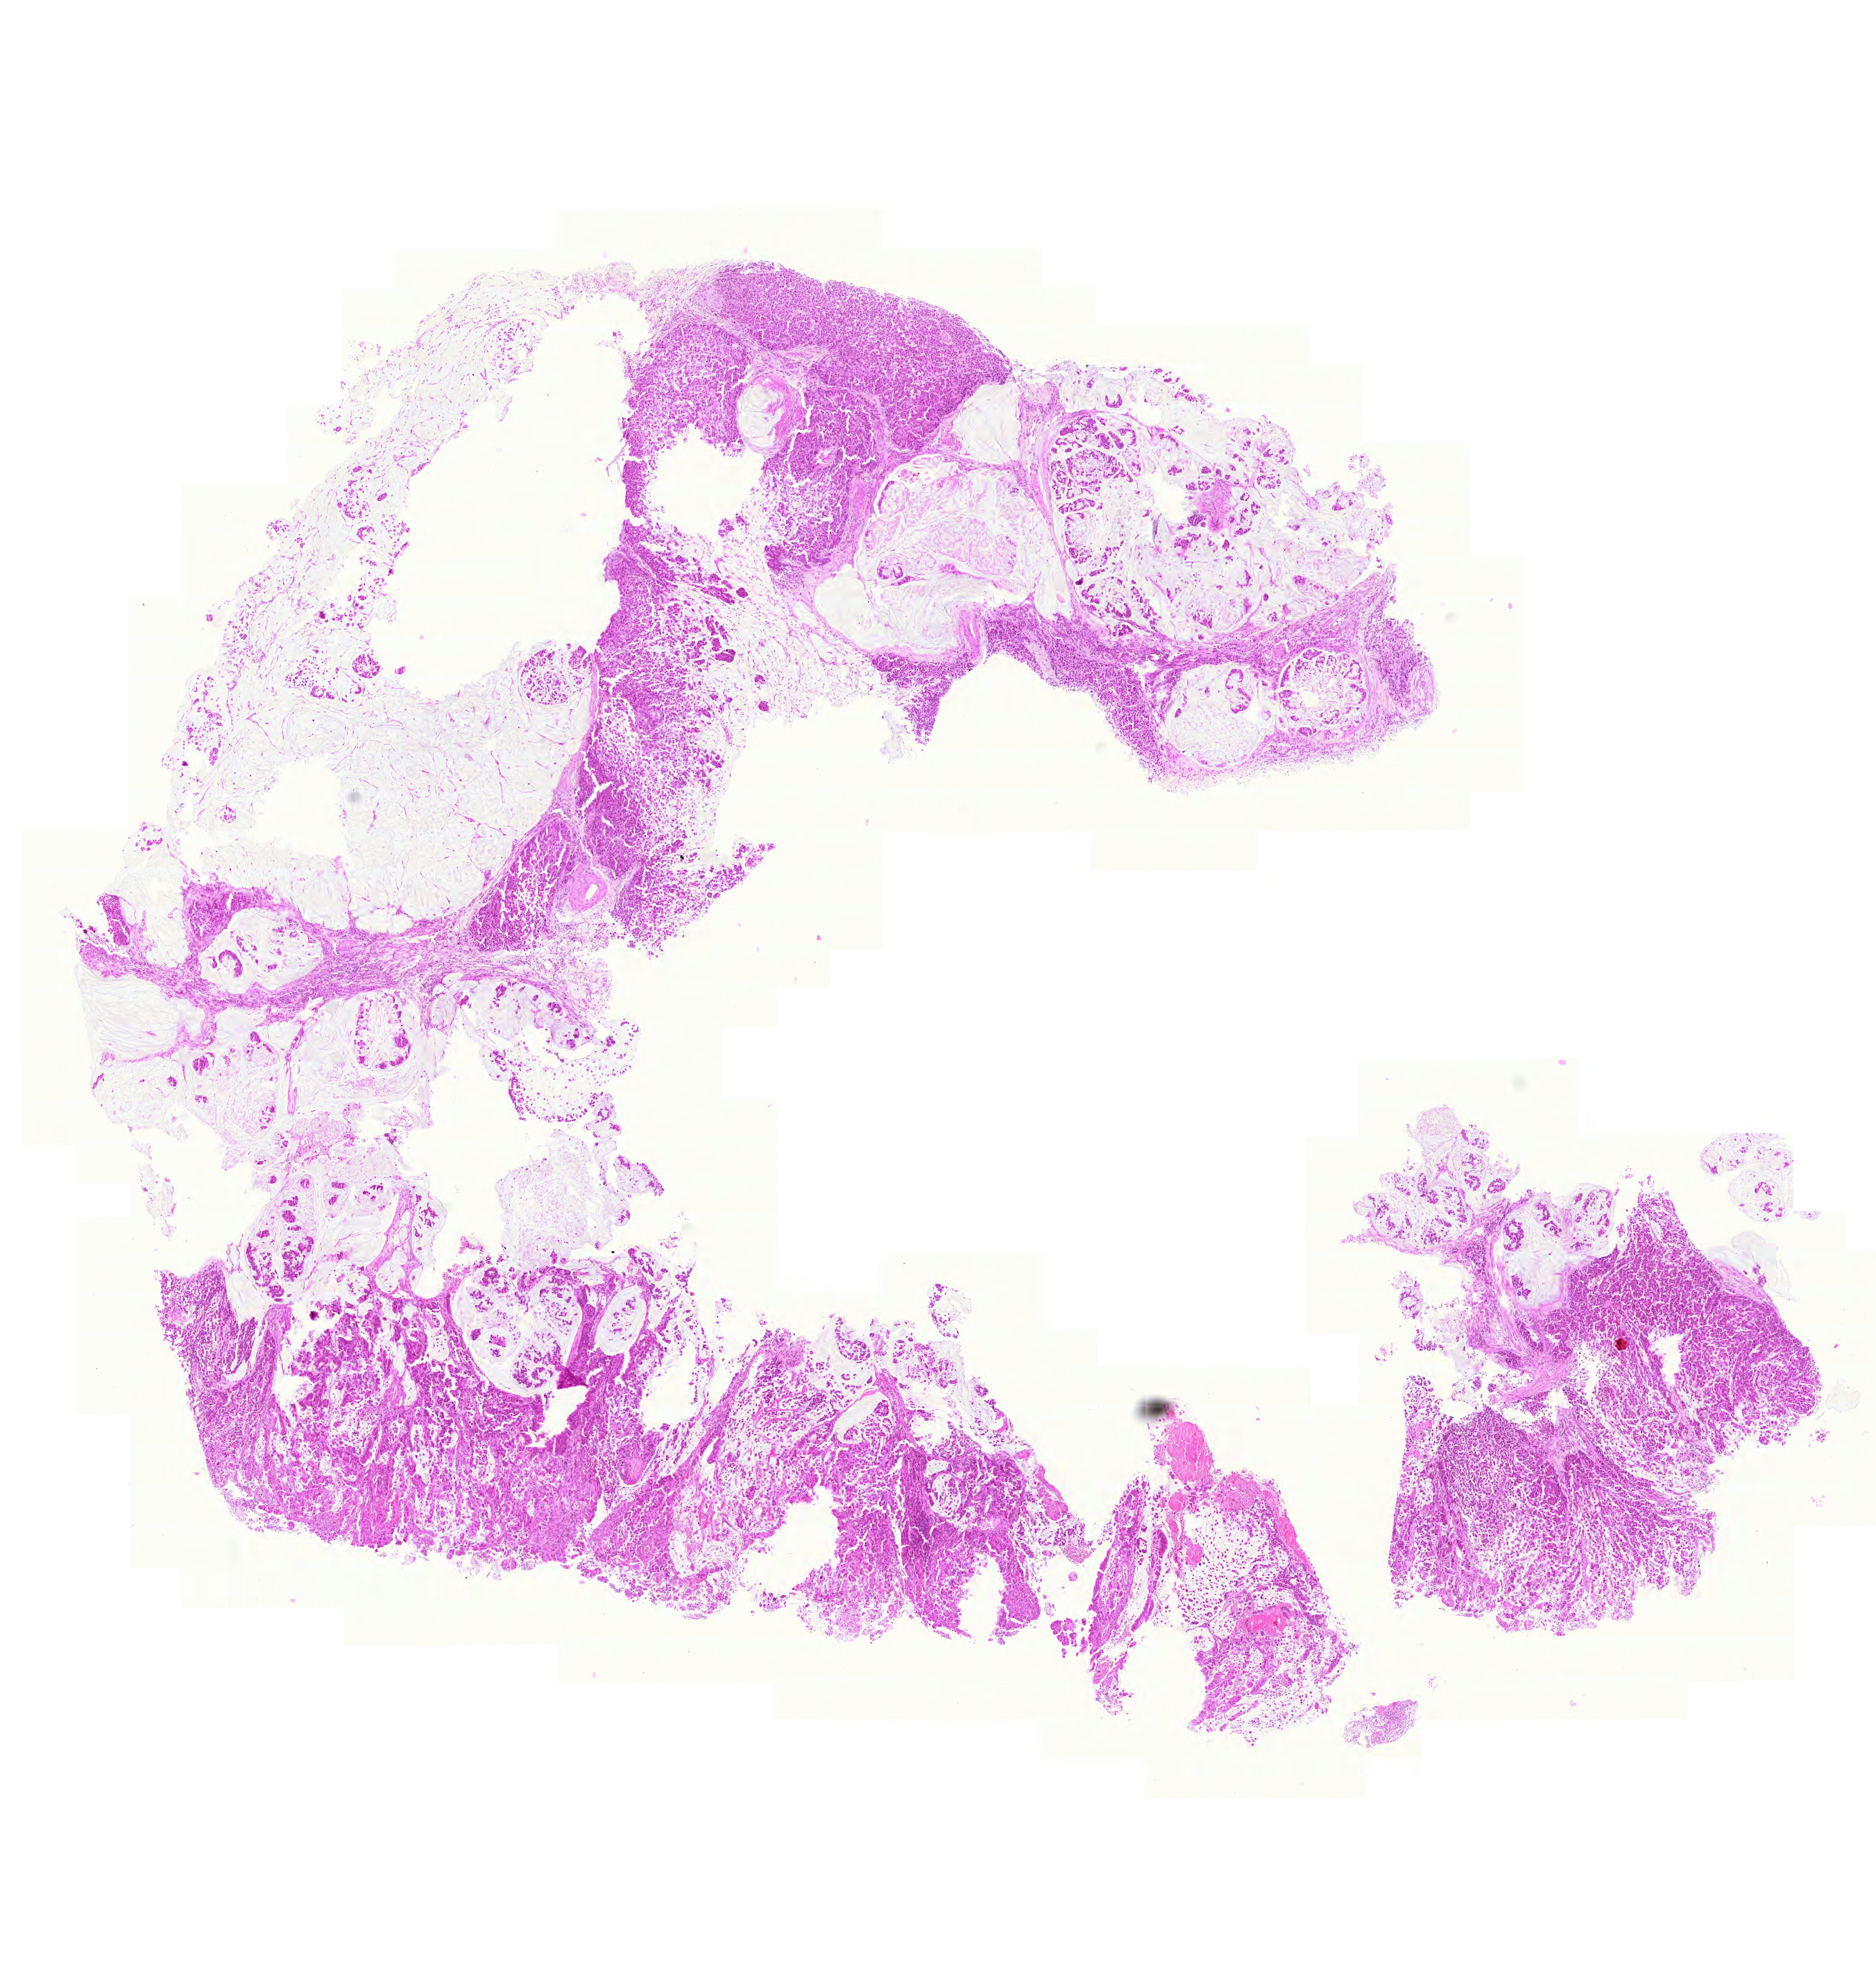
Digitized Hematoxylin and eosin (H&E) stained tissue section (whole slide) — shown as a low-resolution overview of the whole scanned area (about 10.1 x 10.7 mm, from a 20x scan). Formalin-fixed paraffin-embedded (FFPE) diagnostic section. Stomach, primary tumour sample. Male, age 76 years at initial diagnosis. Histologic grade: G3 (poorly differentiated).
- pathologic diagnosis: Adenocarcinoma, intestinal type (body of stomach)
- lymph nodes positive (case pathology): 15 of 37 examined
- AJCC pathologic stage: IIIA